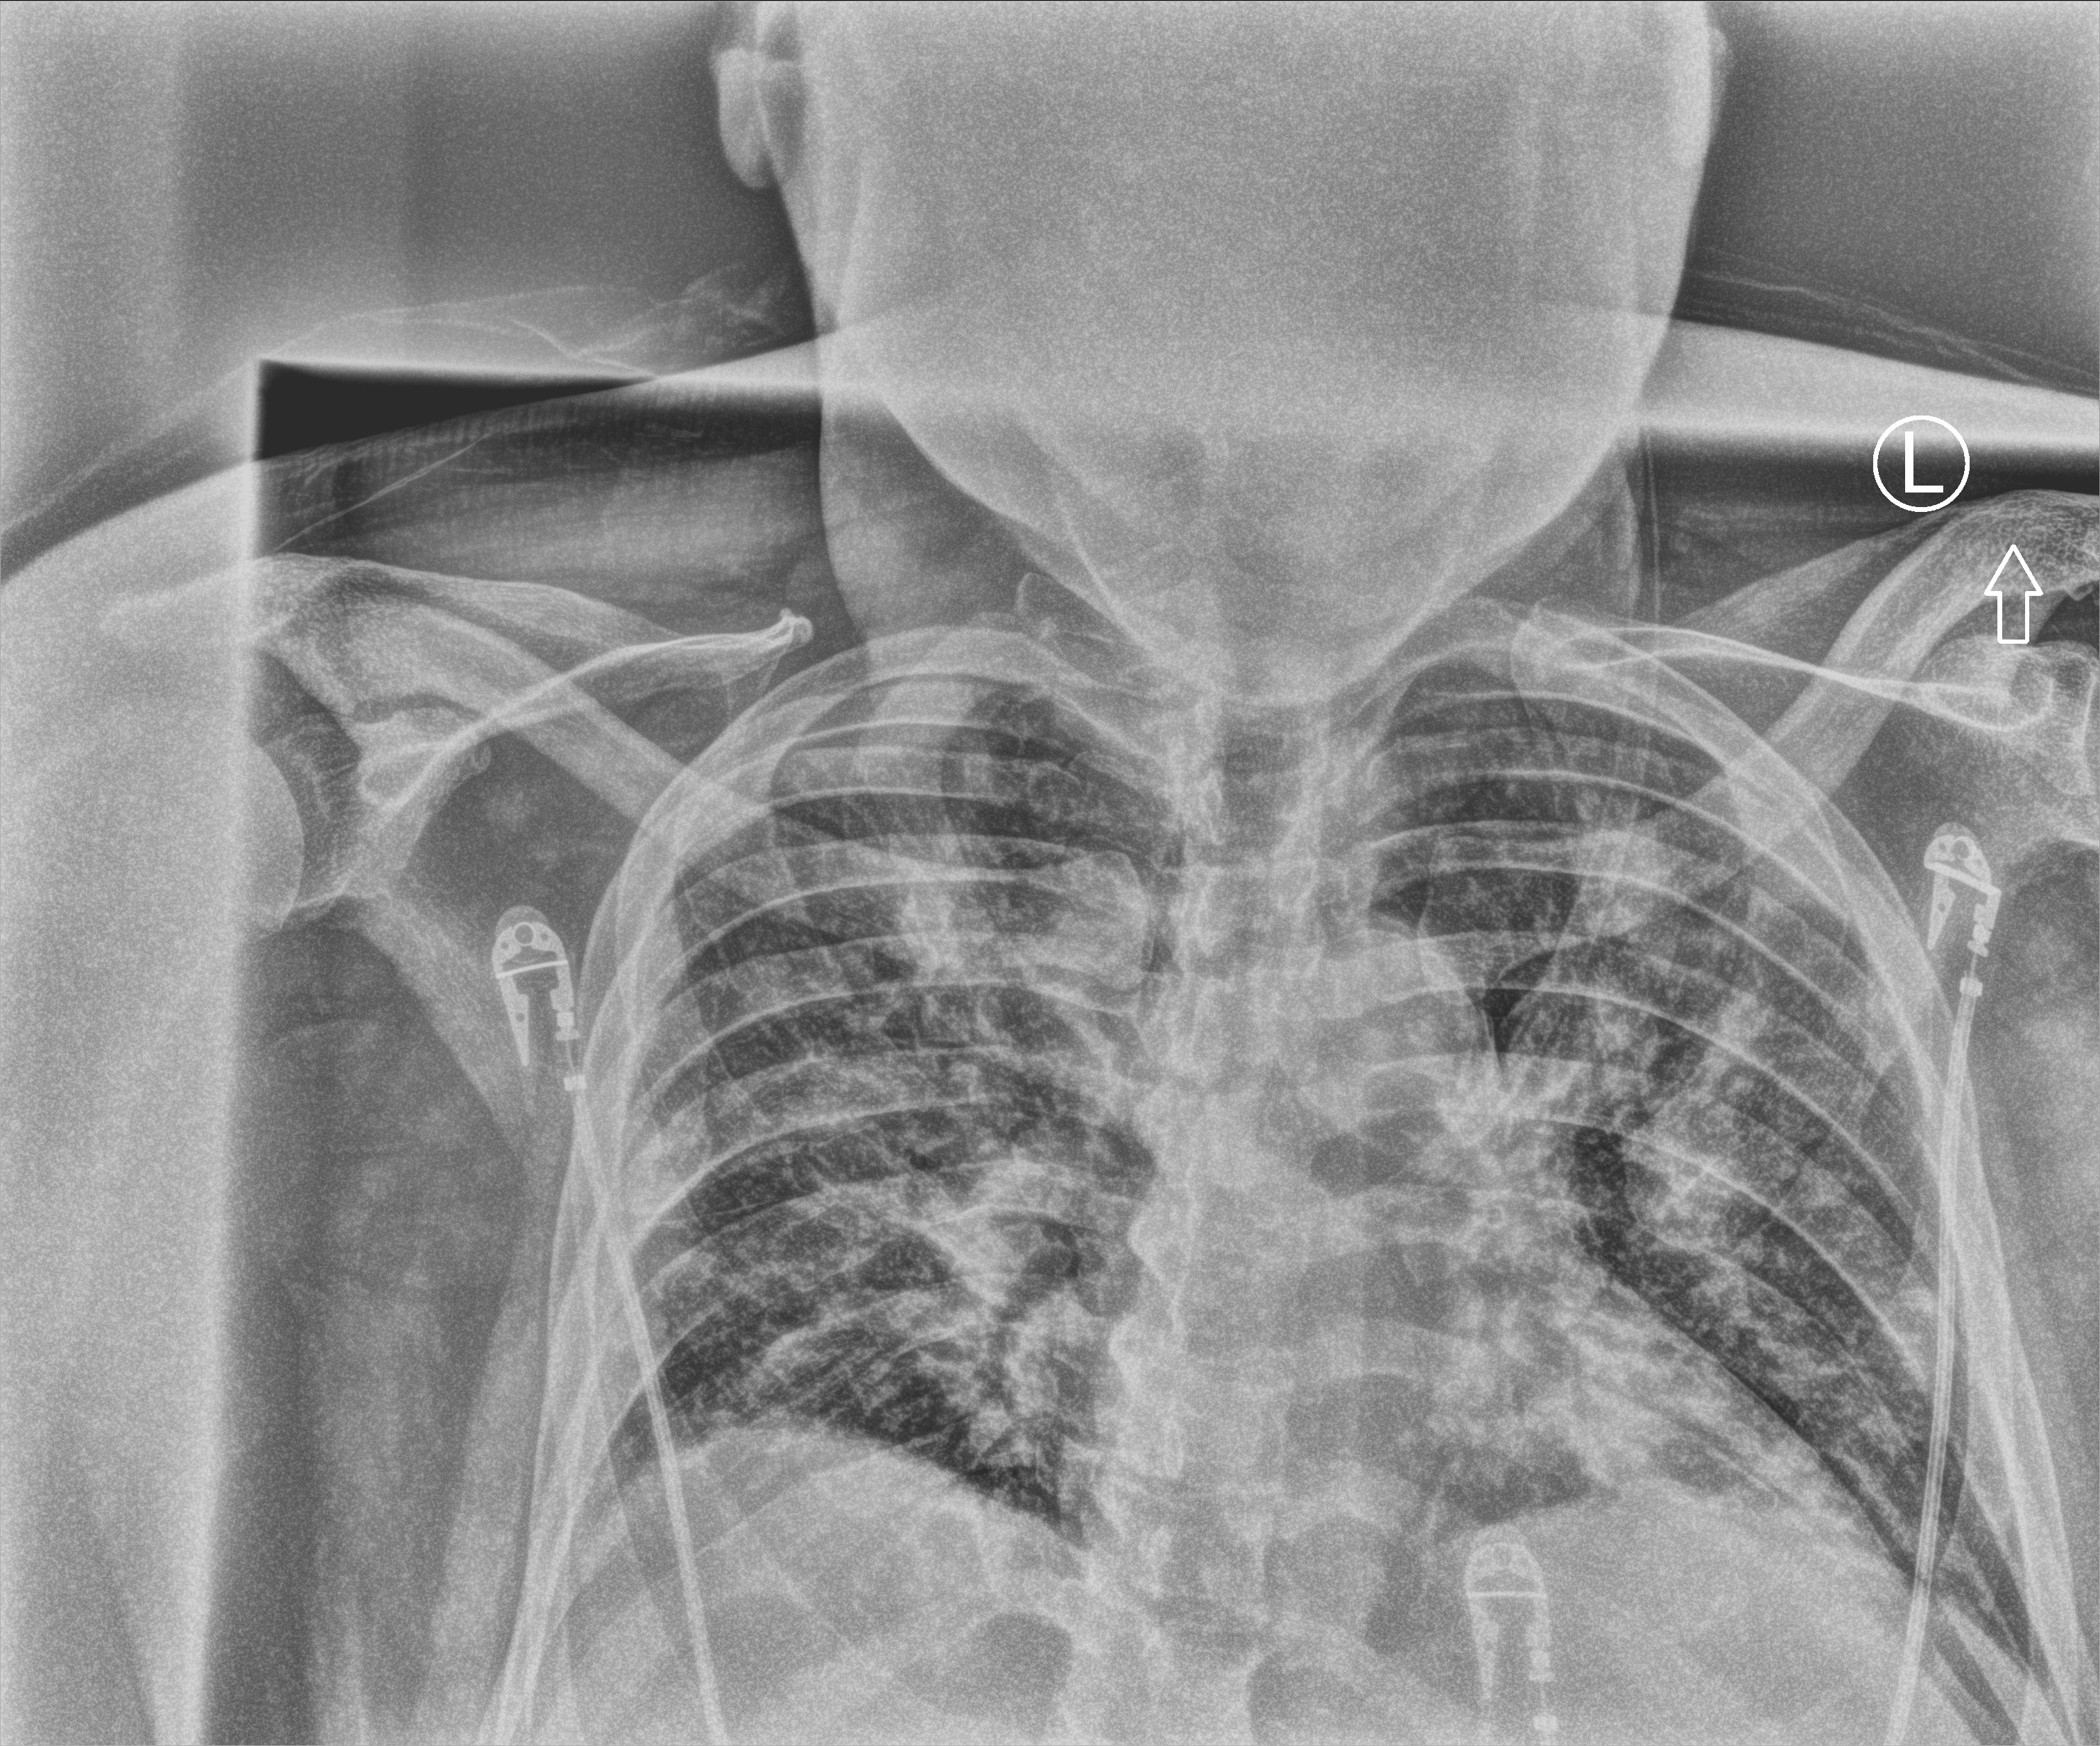
Bedside chest radiograph (computed radiography); anteroposterior (AP) projection. Male patient hospitalised with COVID-19, age 60–74 years.
From the hospital-stay record, not from the radiograph (when in the stay this image was taken is not recorded):
- smoking status (admission record): former
- mechanically ventilated during this hospital stay: no
- length of hospital stay: 7 days